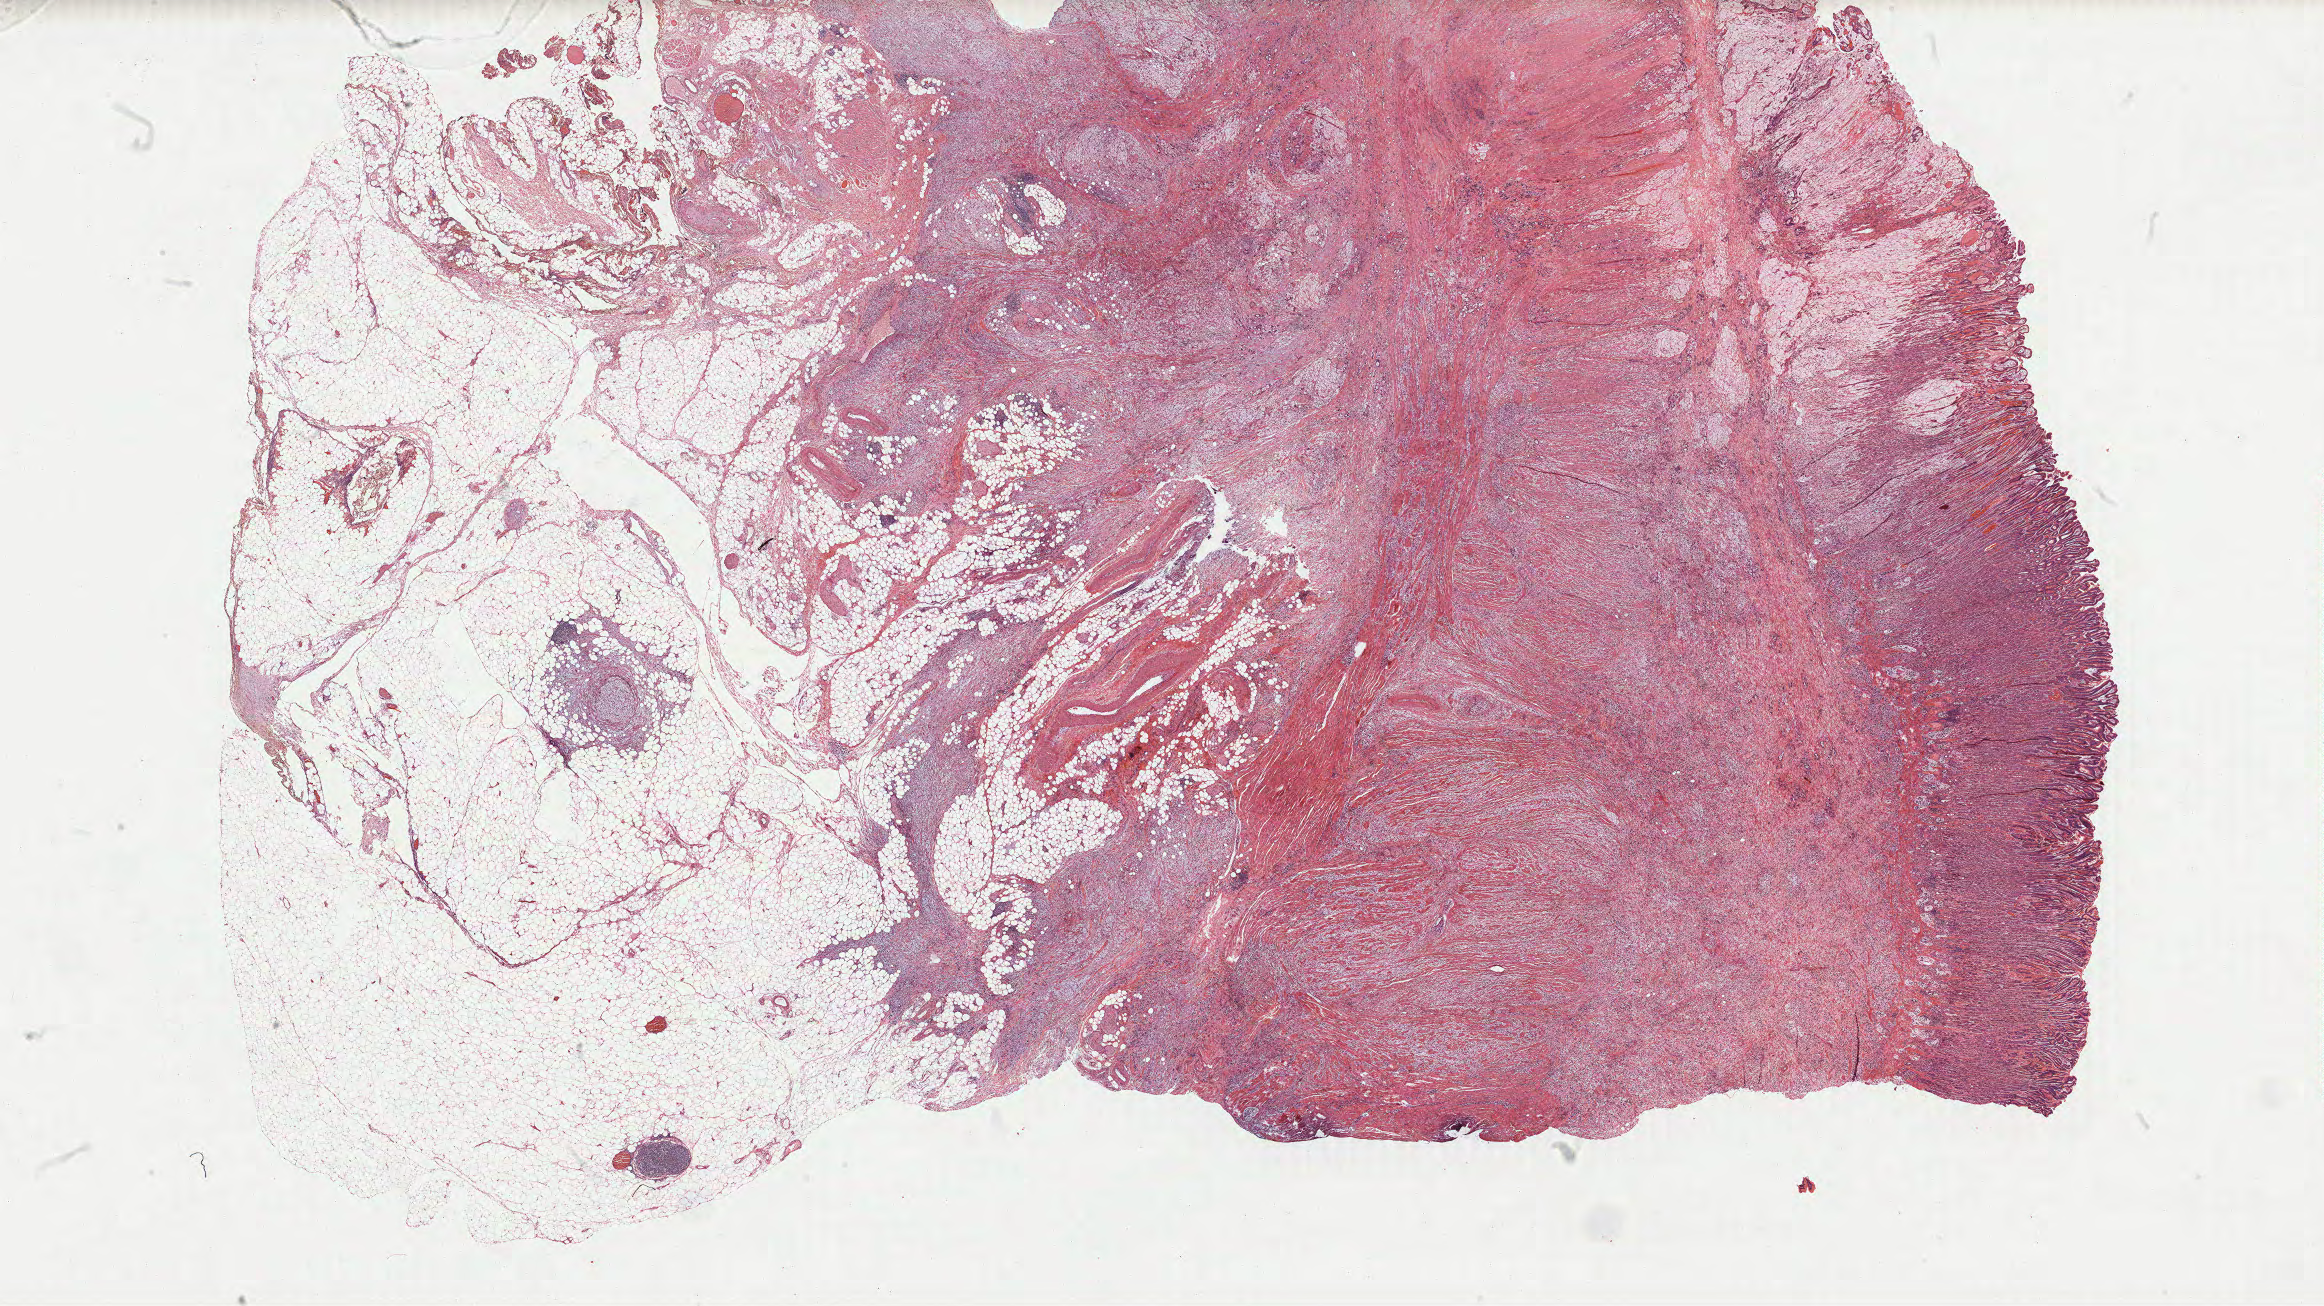
Whole-slide histology image, H&E-stained, low-resolution overview of the scanned area, about 37.4 x 21.0 mm; formalin-fixed paraffin-embedded (FFPE) diagnostic section; primary tumour sample from the stomach. Patient: male, age at initial diagnosis 46 years. Histologic grade: G3 (poorly differentiated).
• lymph nodes positive (case pathology): 5 of 8 examined
• AJCC pathologic stage: IIIA
• diagnosis: Carcinoma, diffuse type (cardia, NOS)